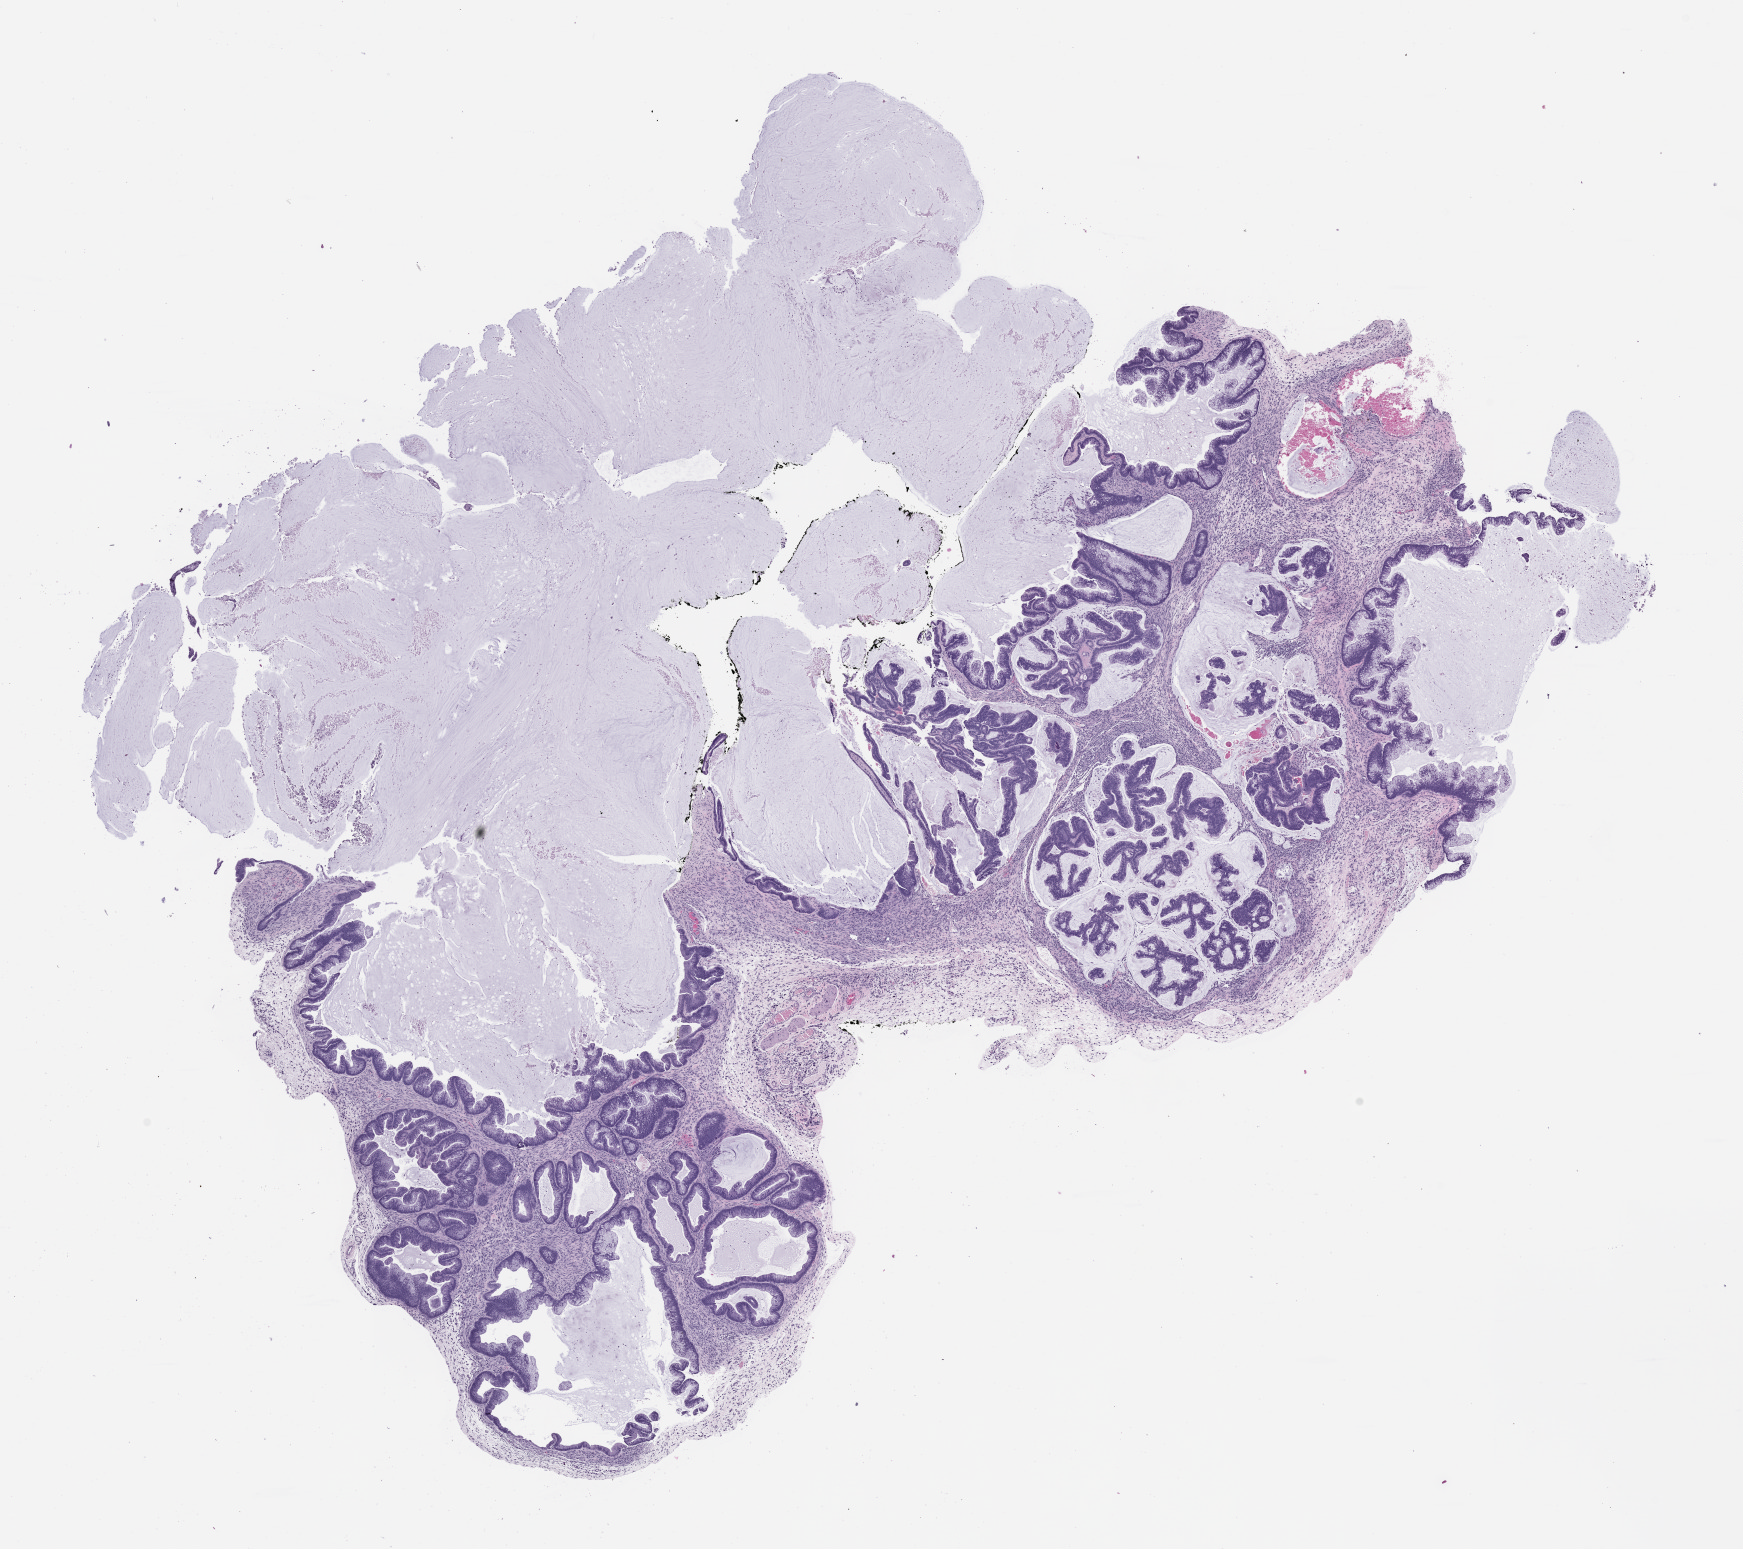
Whole-slide image, hematoxylin and eosin (H&E): patient-derived xenograft (human tumor grown in a mouse), passage 0, whole scanned area (about 14.0 x 12.5 mm) shown as a low-resolution overview; FFPE section; originating tumor site category: colon.
Originating patient diagnosis: Colon Adenocarcinoma.